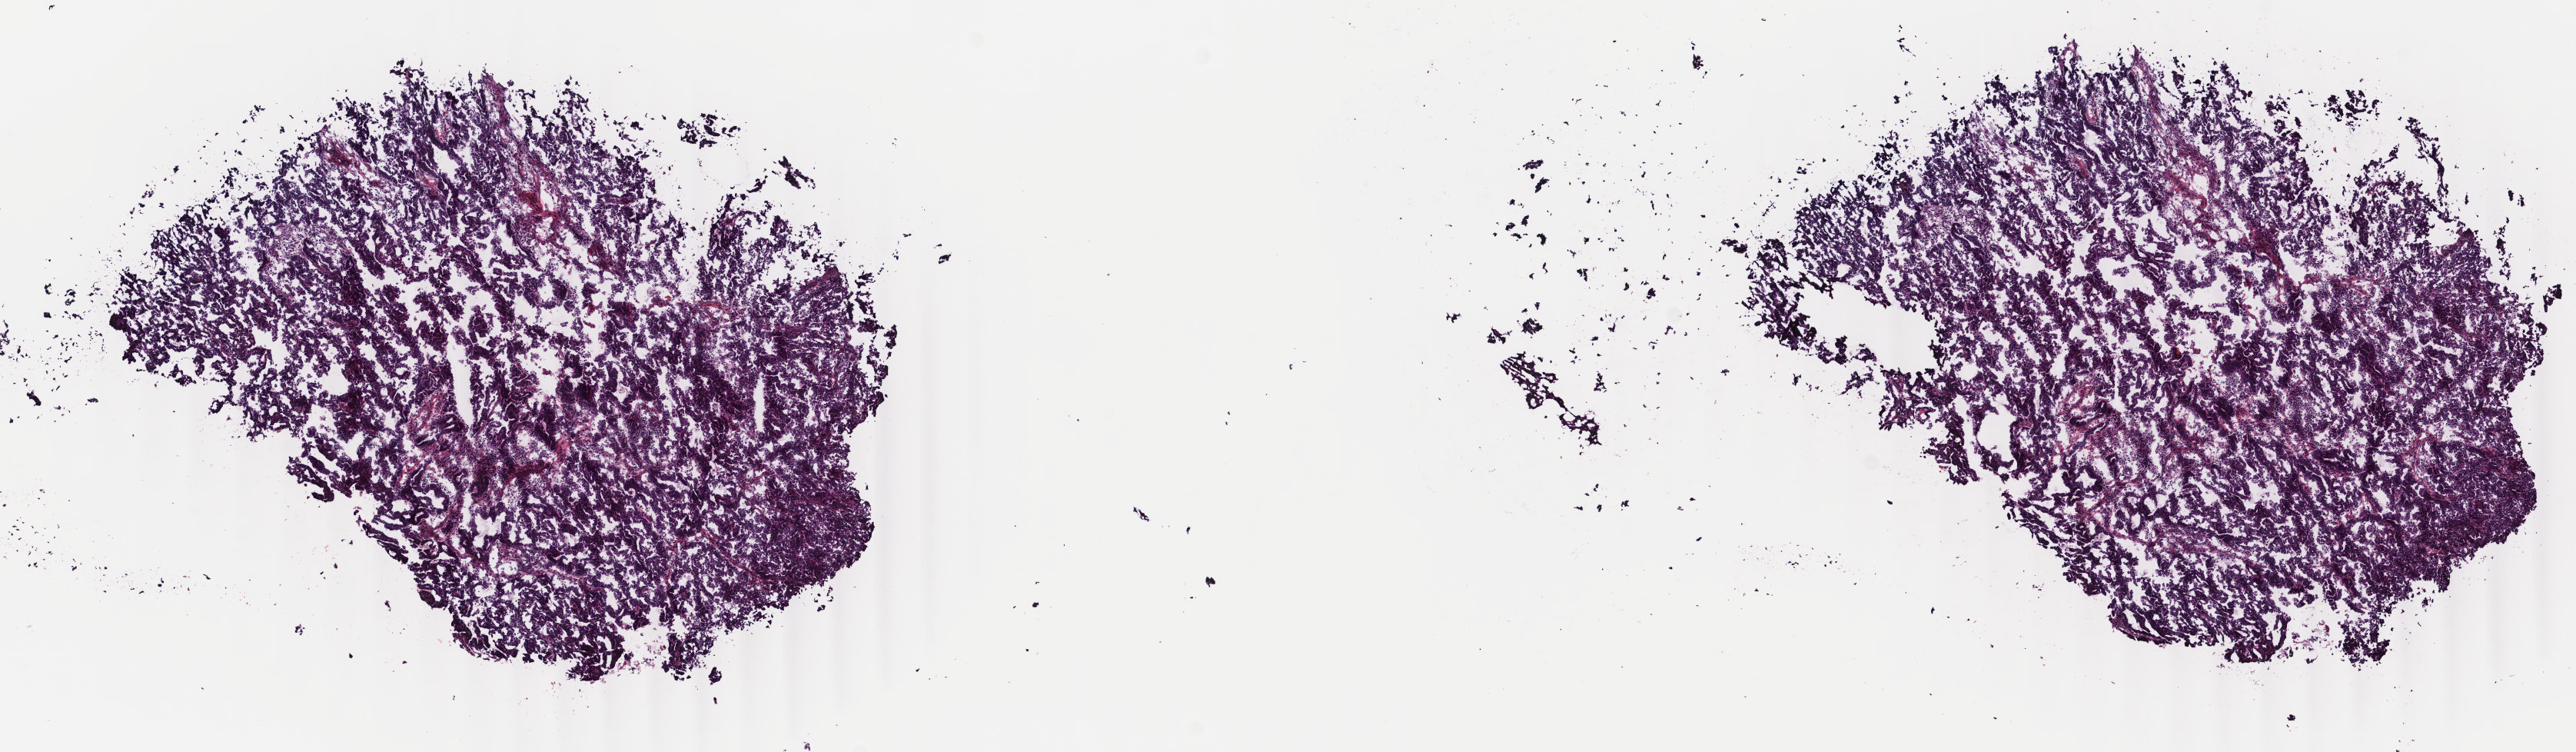
Whole-slide histology image, H&E-stained, low-resolution overview of the scanned area, about 13.3 x 3.9 mm (slide scanned at 40x); frozen section; uterus, primary tumour sample. Female, age 68 years at initial diagnosis. Histologic grade: G1 (well differentiated). Slide review estimates, as recorded: tumour cells 100%, tumour nuclei 85%, normal cells 0%, stromal cells 0%, necrosis 0%. Infiltration values recorded for this section: lymphocyte infiltration 0%, monocyte infiltration 0%, neutrophil infiltration 0%.
- FIGO stage: IA
- pathologic diagnosis: Endometrioid adenocarcinoma, NOS (endometrium)